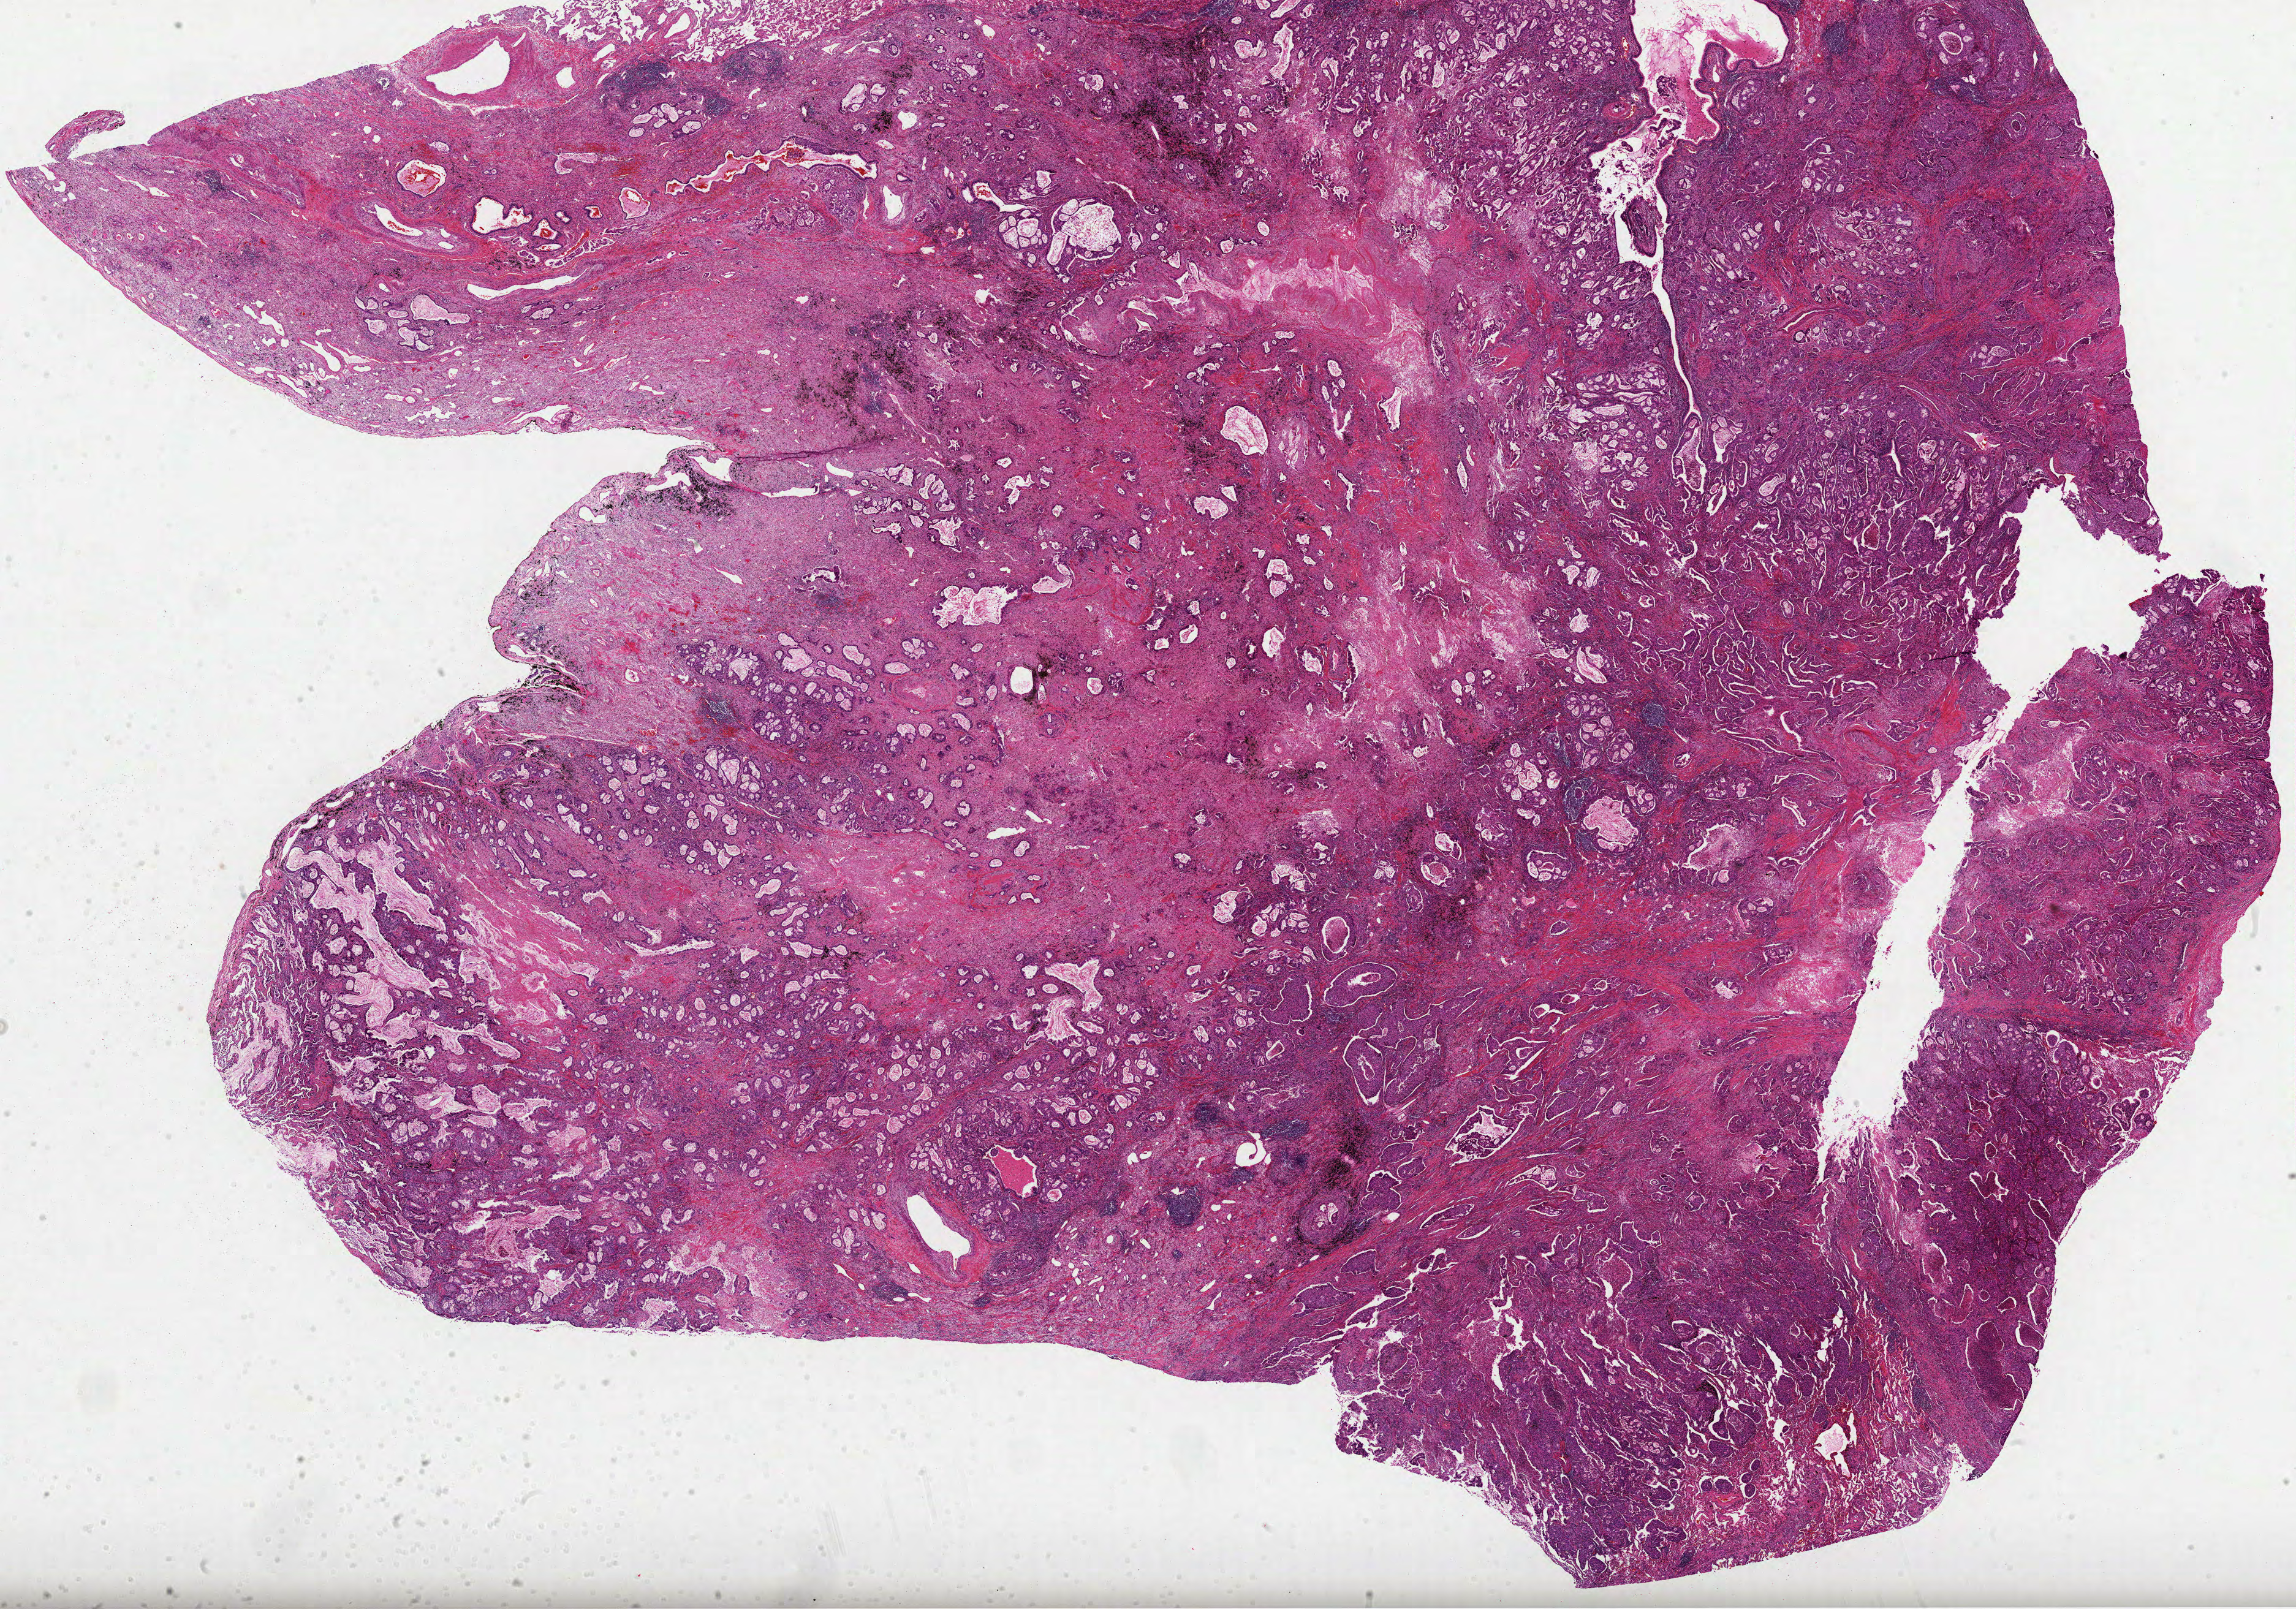
H&E whole-slide image, low-resolution overview of the scanned area, about 30.2 x 21.2 mm, formalin-fixed paraffin-embedded (FFPE) diagnostic section, sample: primary tumour, lung. Patient: male, age at initial diagnosis 77 years.
* TNM: T3 N2 M0
* diagnosis: Adenocarcinoma, NOS (upper lobe, lung)
* laterality: left
* AJCC pathologic stage: IIIA (4th edition)